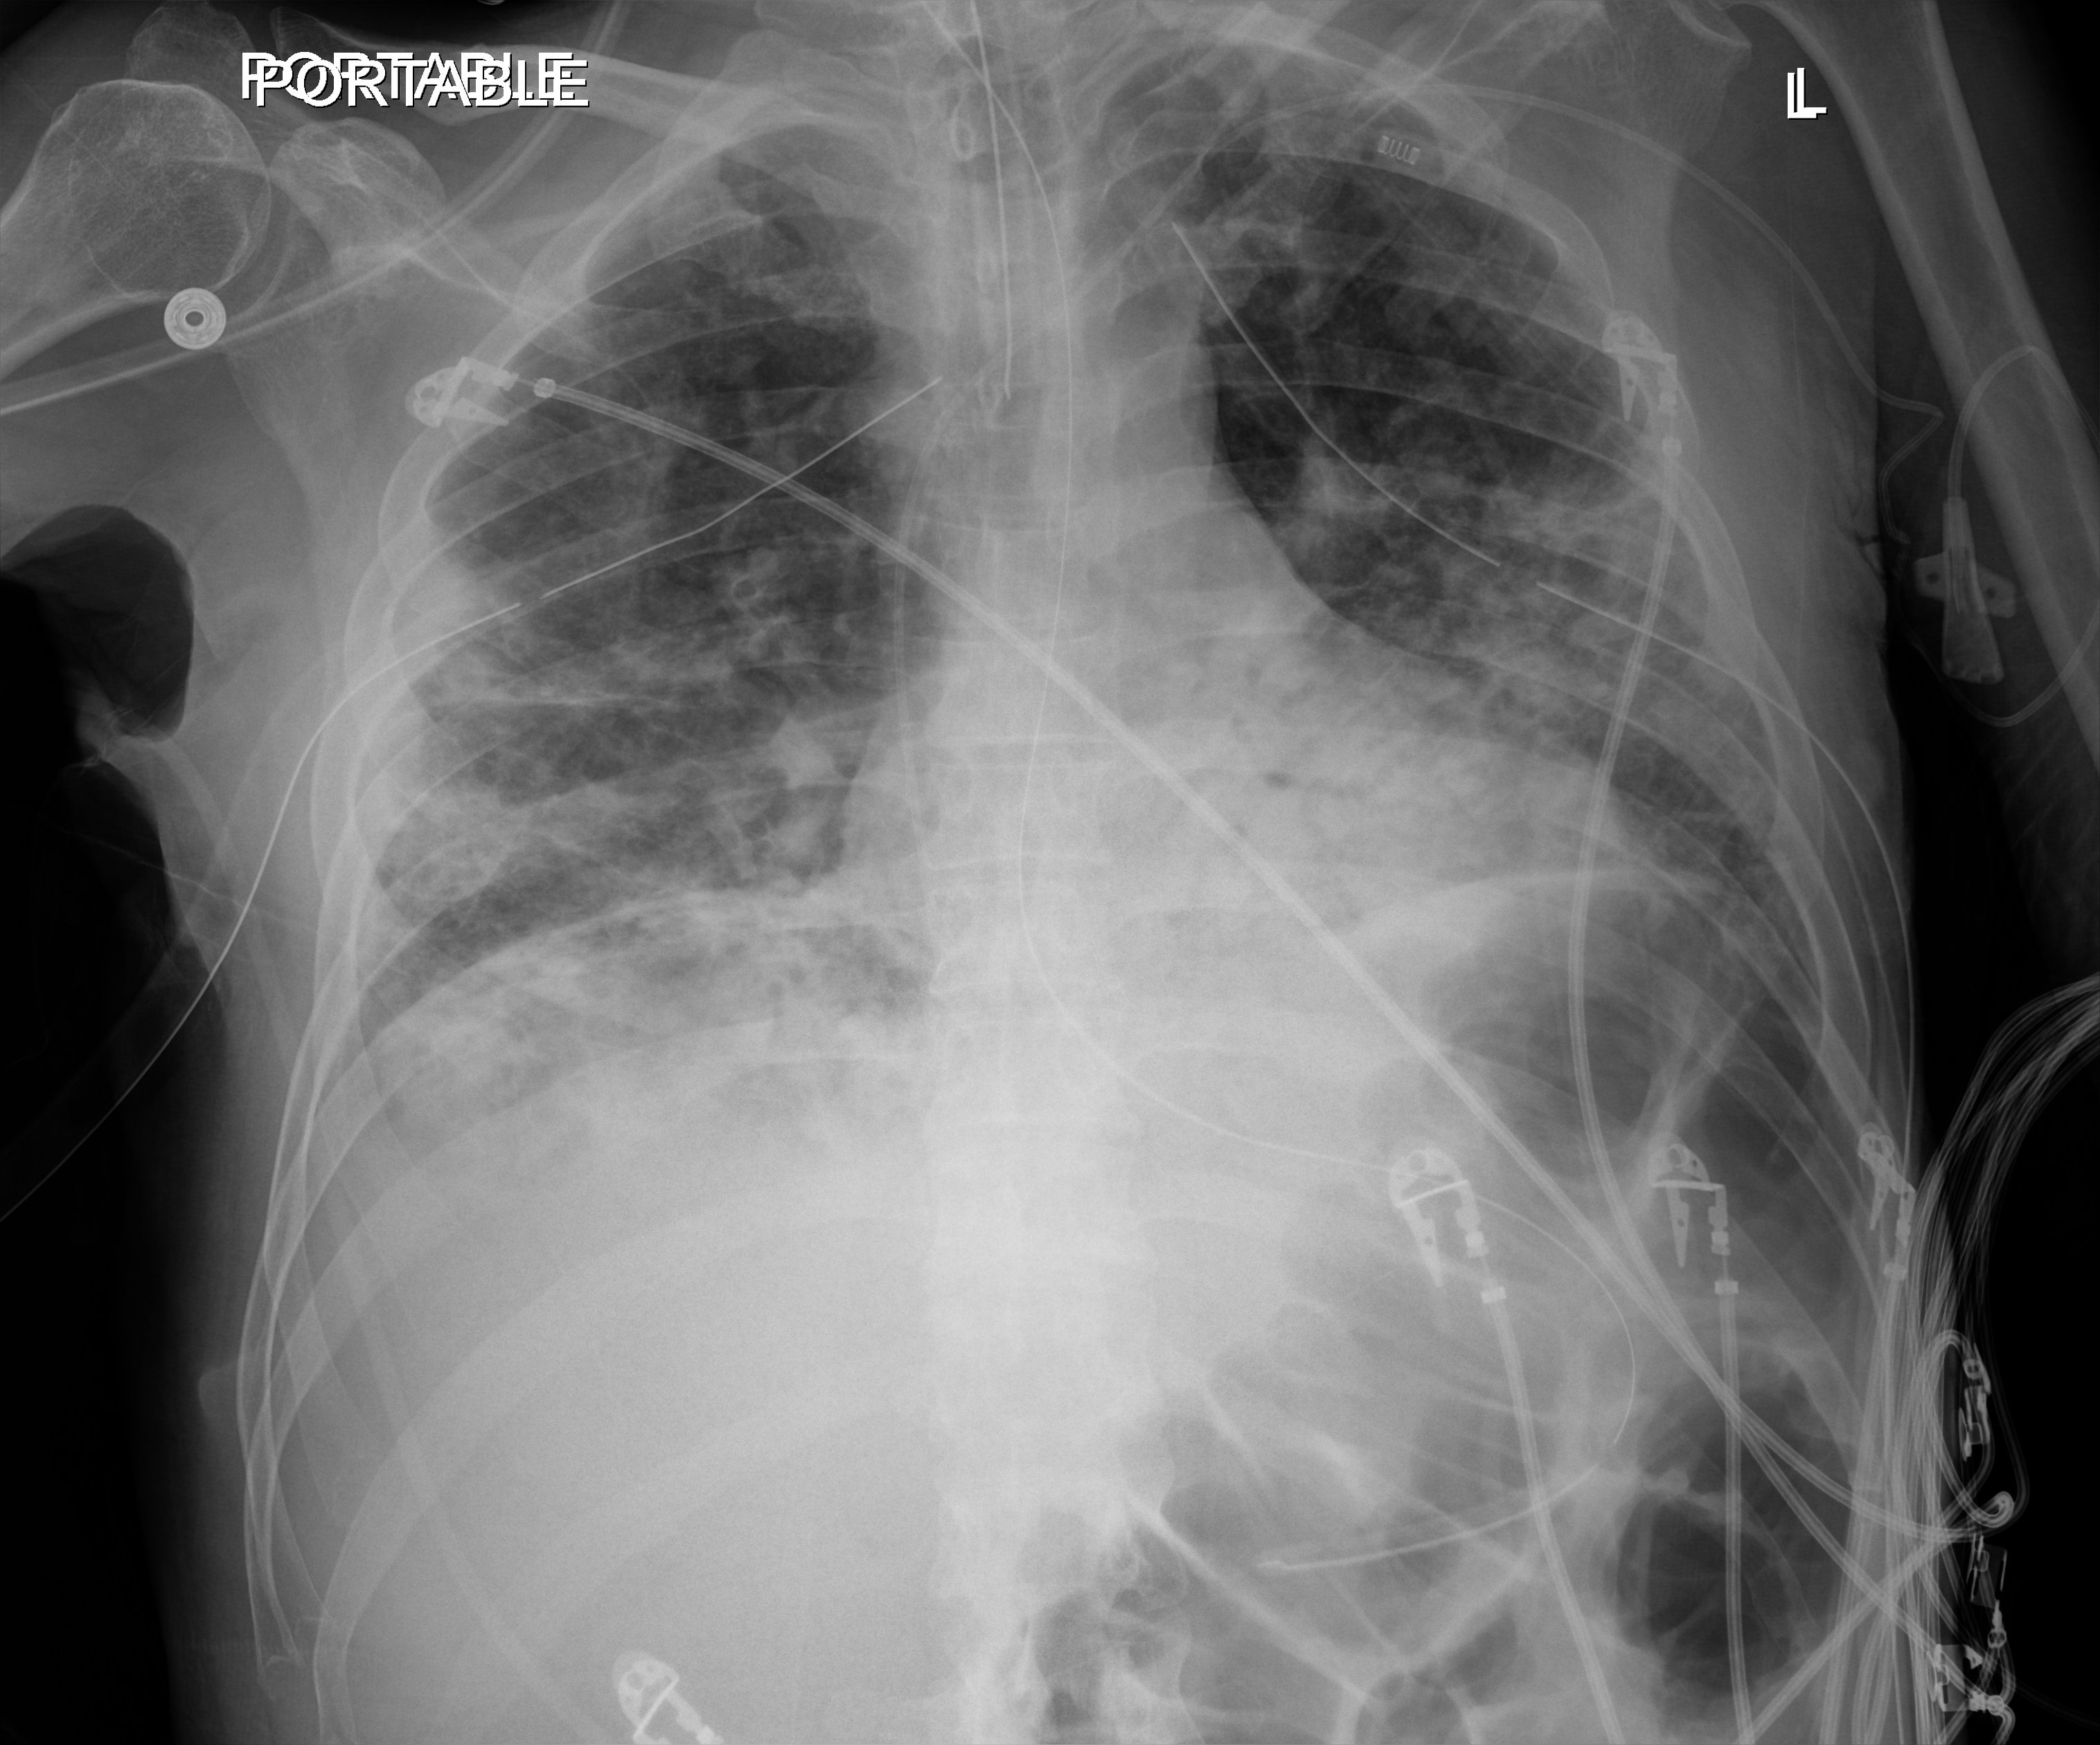
Chest X-ray (portable). Male patient hospitalised with COVID-19, age 18–59 years.
Admission-level facts for this patient (not findings on this image; timing relative to this image not recorded): COPD (admission record): no; smoking status (admission record): never; mechanically ventilated during this hospital stay: yes.